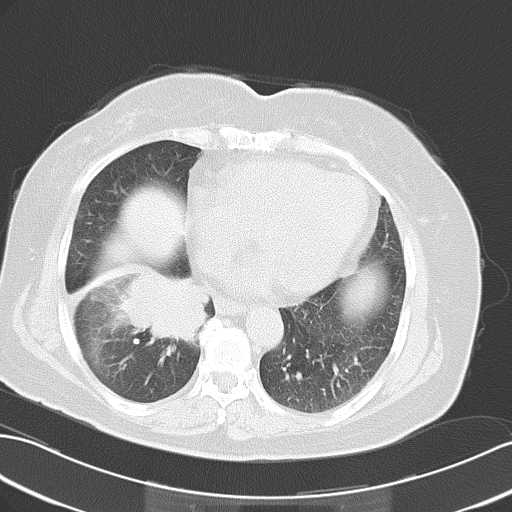
Chest CT, one axial slice. Reconstruction kernel B70f. 120 kVp. Lung window (W 1500 / L -600 HU). 512 × 512 image matrix, field of view 353 × 353 mm. Patient: female, 63 years. From the clinical record (not read from this slice): clinical TNM (as recorded): T3 N0 M0.
Outlined on this slice (rectangle marked by the reading radiologist):
- lung tumour (recorded histology: adenocarcinoma): bounding box (x1, y1, x2, y2) in pixels: (118, 268, 212, 350)